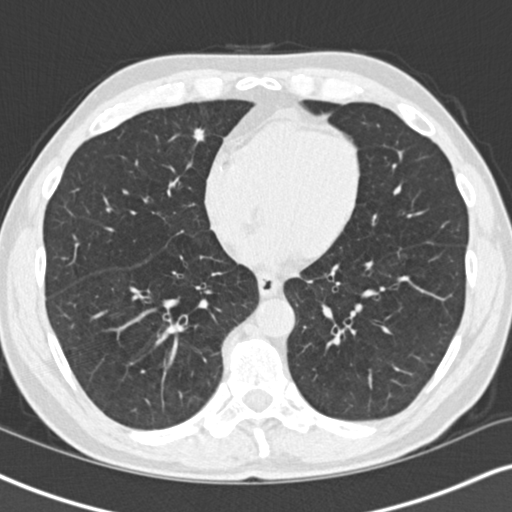
Low-dose screening chest CT, one axial slice. Slice 44 of 148 in the series (ordered by position). Reconstruction kernel B30f. 120 kVp. Lung window (W 1500 / L -600 HU). 2 mm slice thickness. 512 × 512 image matrix, field of view 328 × 328 mm.
Structures marked on this image (expert manual segmentation):
- lesion 1 (tumor, middle lobe of right lung): bounding box (x1, y1, x2, y2) in pixels: (193, 128, 204, 143)